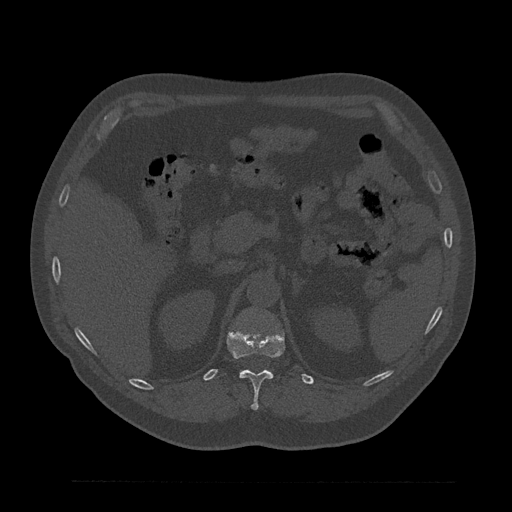
CT including the spine, one axial slice. Position 217 of 797 along the scan axis. Reconstruction kernel Br40s/3. Bone window (W 1800 / L 400 HU). 0.5 mm slice thickness. 512 × 512 image matrix. Patient: male, 61 years. Case-level facts recorded for this patient, not image findings: primary cancer: prostate.
Outlined on this slice (semi-automatically segmented with operator editing):
- T12 vertebra: bounding box <227,330,285,410> (left, top, right, bottom; pixels)